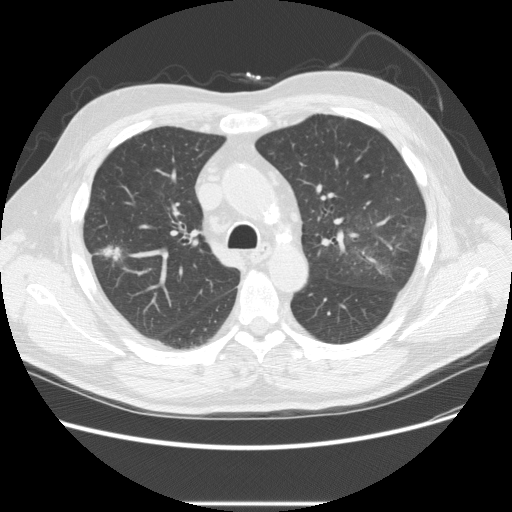
Low-dose screening chest CT, one axial slice; slice 157 of 233 in the series (ordered by position); reconstruction kernel STANDARD; 120 kVp; lung window (W 1500 / L -600 HU); 2.5 mm slice thickness; 512 × 512 image matrix.
Outlined on this slice (outlined manually by an expert reader):
- lesion 2 (tumor, upper lobe of right lung): box from (x=100, y=246) to (x=122, y=261) px